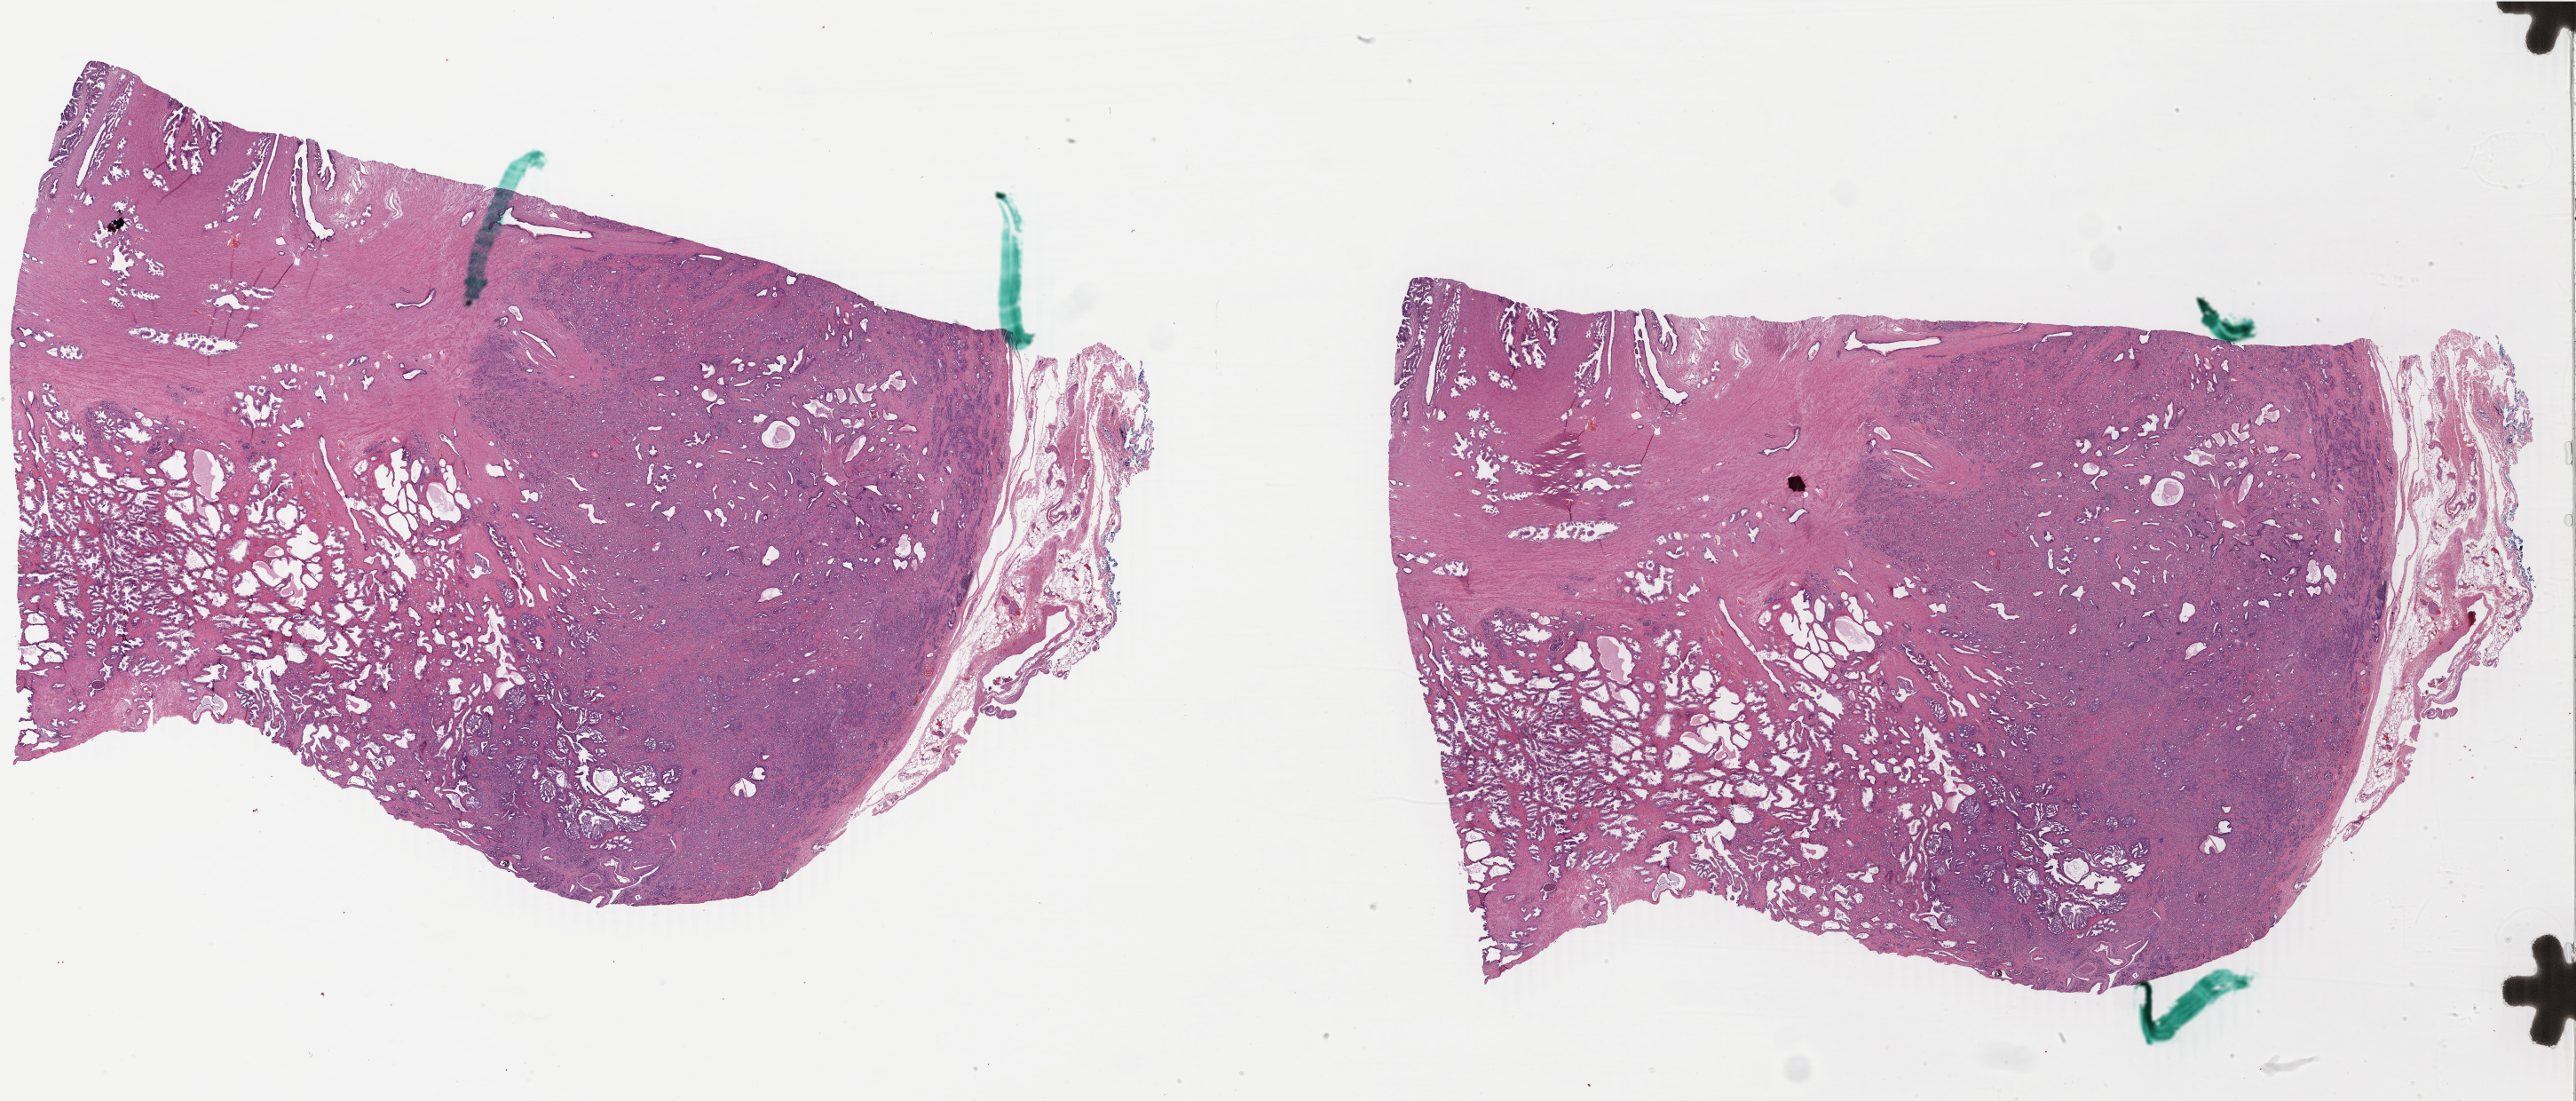
Hematoxylin and eosin (H&E) stained whole-slide image, shown as a low-resolution overview of the whole scanned area (about 46.2 x 19.7 mm, slide scanned at 40x). FFPE section. Sample: primary tumour, prostate. Male, age 68 years at initial diagnosis. Gleason score: 7 (4+3).
Histologic diagnosis: Adenocarcinoma, NOS (prostate gland). Laterality: bilateral.